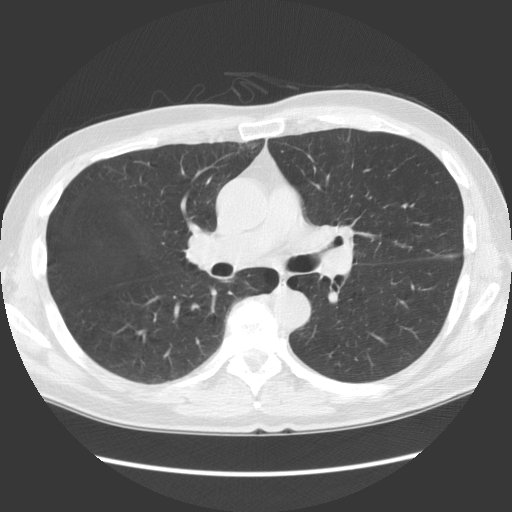
Low-dose screening chest CT, one axial slice; position 76 of 136 along the scan axis; 140 kVp; lung window (W 1500 / L -600 HU); 512 × 512 image matrix.
Structures marked on this image (outlined manually by an expert reader):
- lesion 1 (tumor, hilum of left lung): bounding box <338,226,355,244> (left, top, right, bottom; pixels)